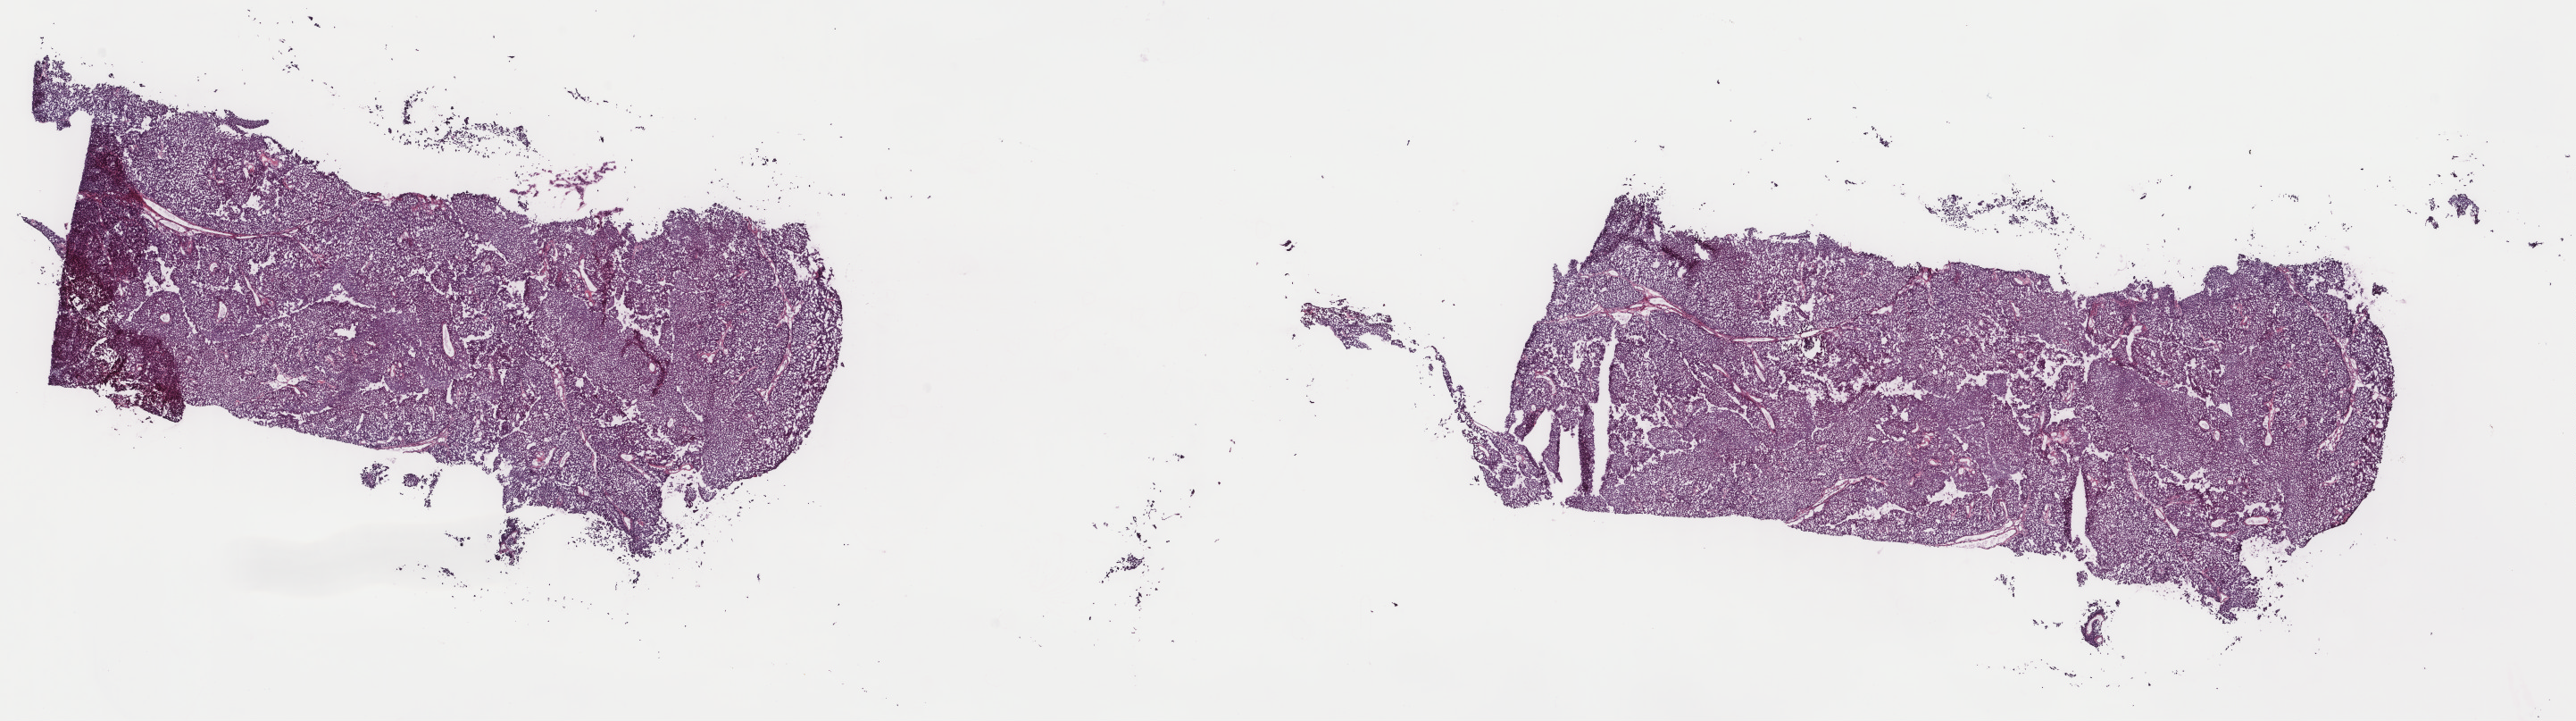
Hematoxylin and eosin (H&E) stained whole-slide image, whole scanned area (about 22.9 x 6.4 mm) shown as a low-resolution overview, frozen section from the top of the tissue portion, primary tumour sample from the bladder. Male, age 42 years at initial diagnosis. Histologic grade: low grade. Slide review estimates, as recorded: tumour cells 100%, tumour nuclei 85%, normal cells 0%, stromal cells 0%, necrosis 0%. Infiltration values recorded for this section: lymphocyte infiltration 1%, monocyte infiltration 0%, neutrophil infiltration 0%.
Histologic diagnosis: Papillary transitional cell carcinoma. AJCC pathologic stage: II (7th edition). TNM: T2 N0 M0.